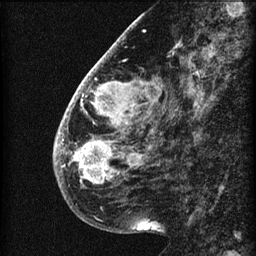
Breast MRI (dynamic contrast-enhanced), one sagittal slice; position 20 of 60 along the scan axis; 3 images stored at this slice position (order not interpretable as contrast timing); 1.5 T; TE 4.2 ms, TR 22.7 ms; 2 mm slice thickness; 256 × 256 image matrix, field of view 180 × 180 mm. Female patient, age 48 years. Case-level facts recorded for this patient, not image findings: setting: breast cancer imaged before/during neoadjuvant chemotherapy; receptor status: triple-negative.
Structures marked on this image (semi-automatically segmented with operator editing):
- analysis volume of interest (the breast-tissue region the enhancement analysis was run in; not a lesion): box from (x=54, y=30) to (x=173, y=207) px
- tumour enhancement mask (voxels above the 90 % enhancement threshold inside the analysis volume of interest): (x=55, y=61)–(x=135, y=185)